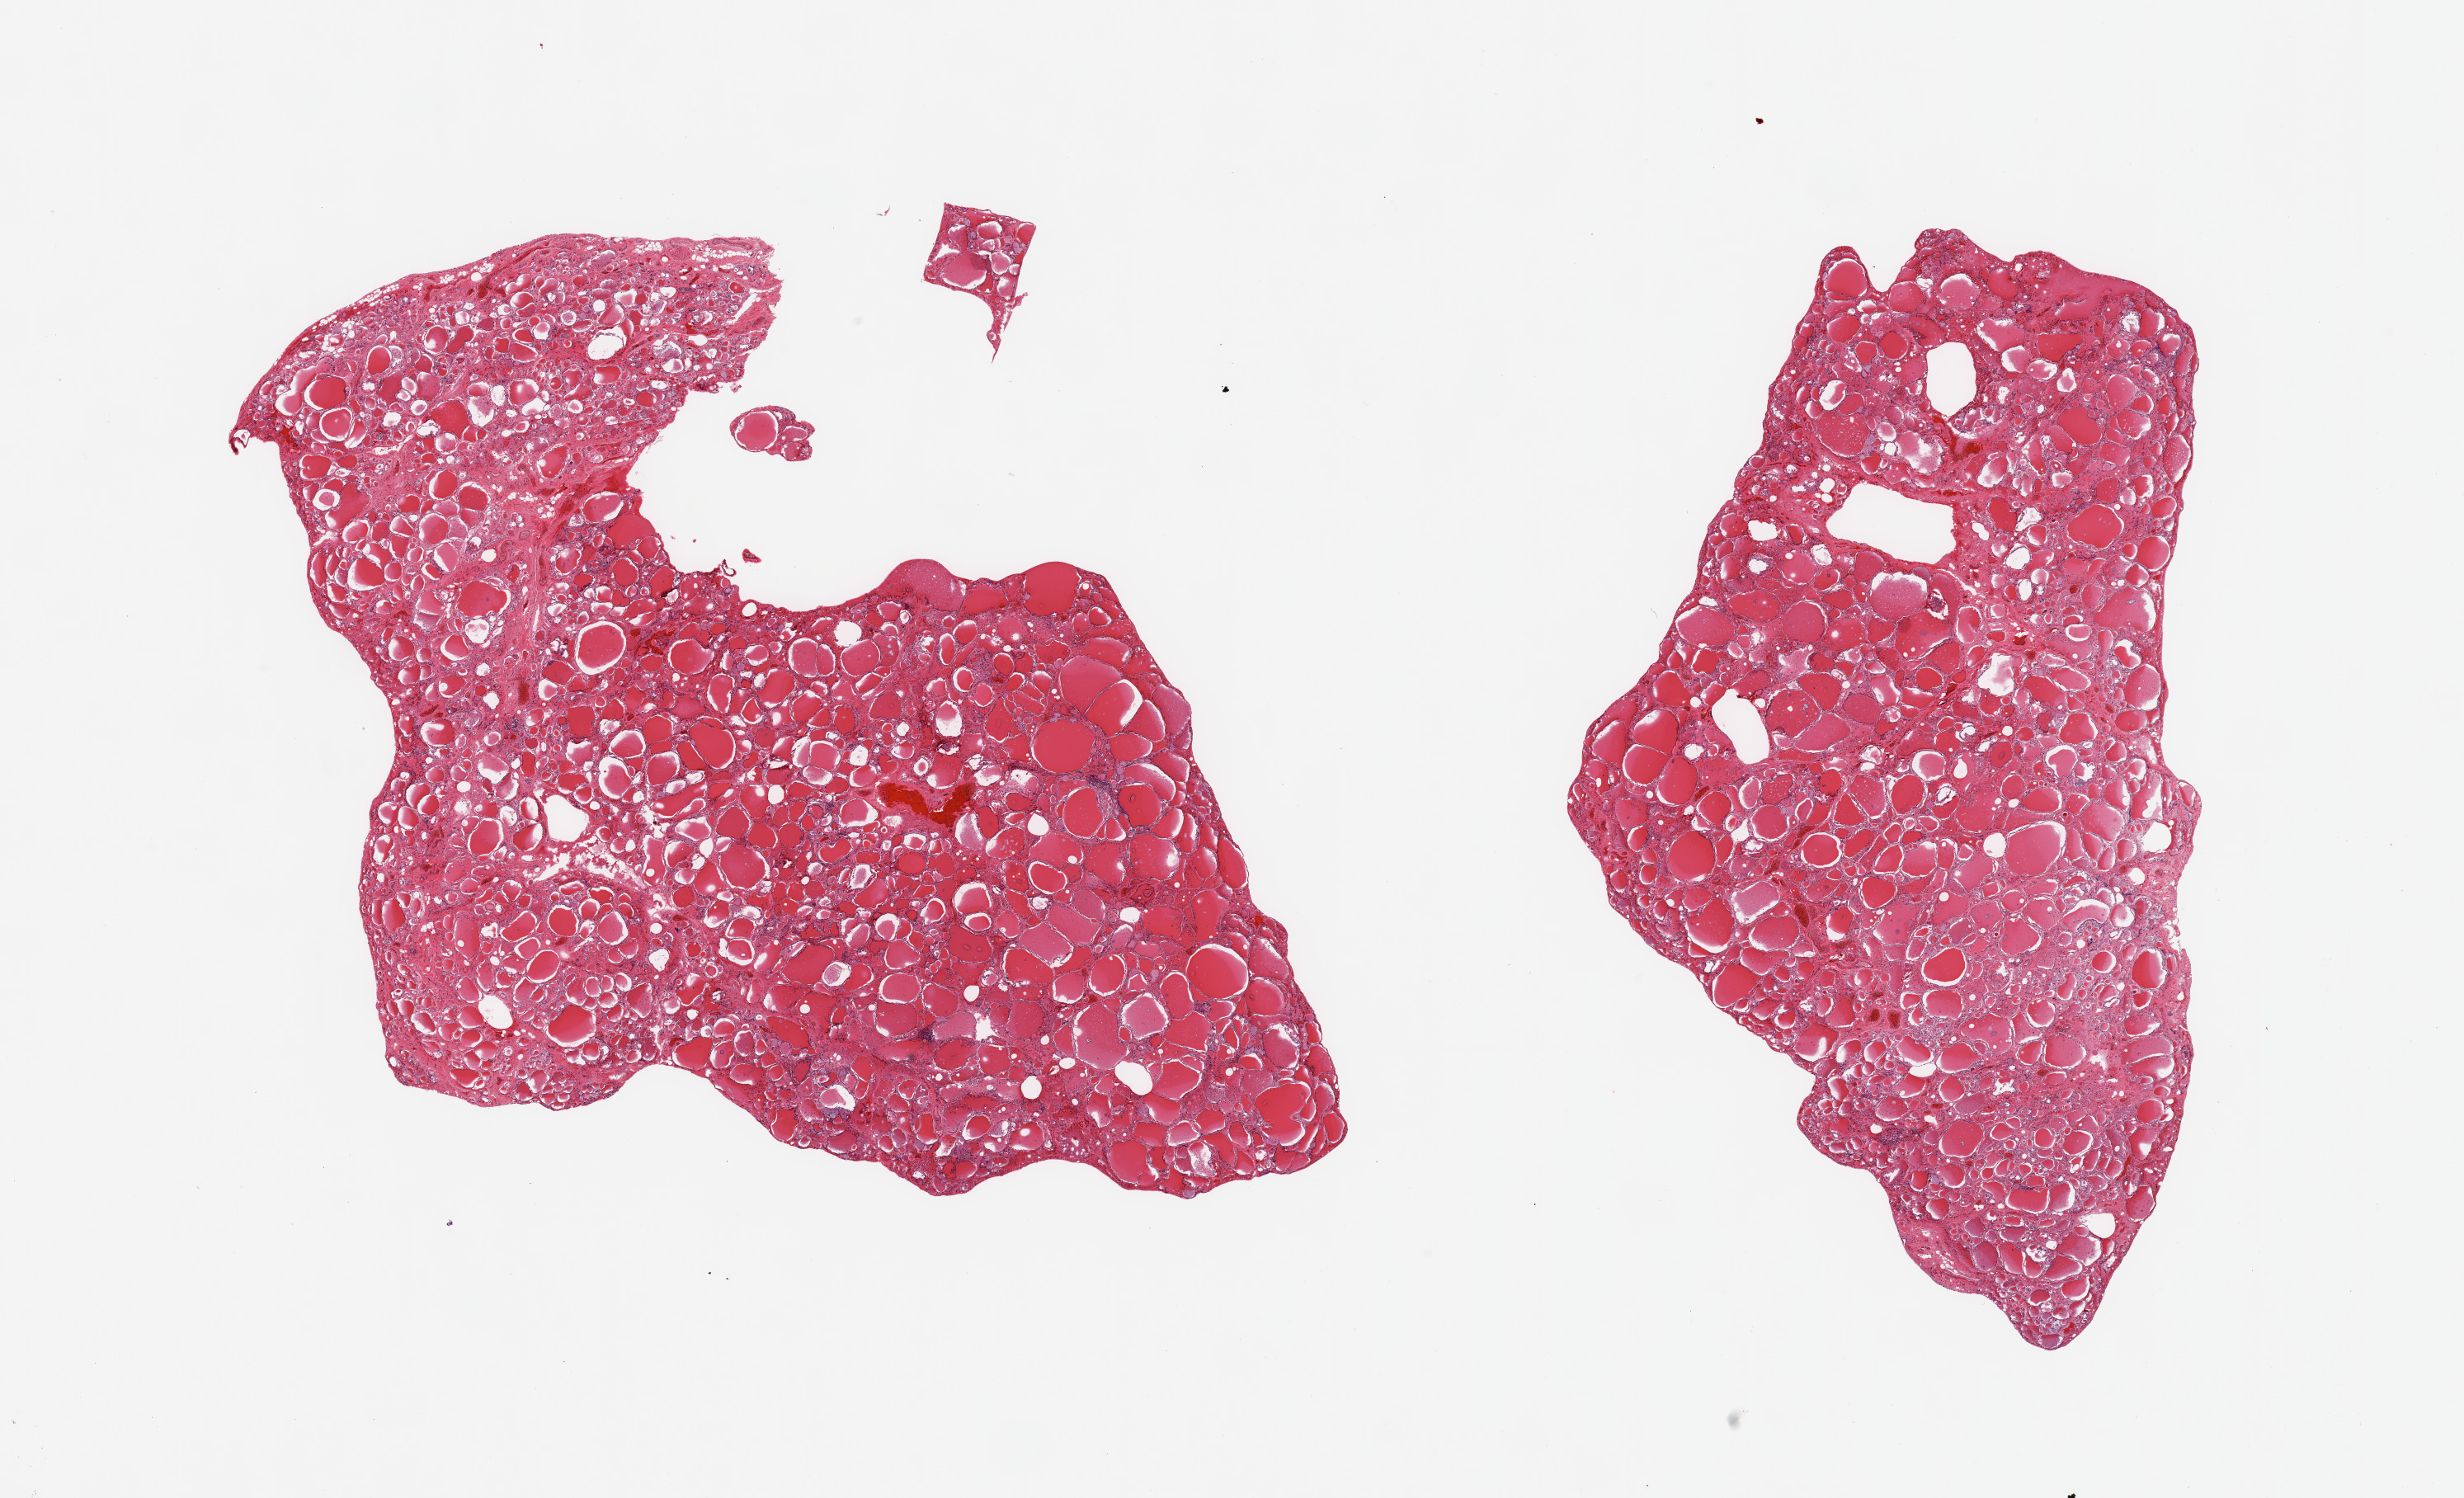
Digitized haematoxylin and eosin-stained section, low-resolution overview of the scanned area, about 23.6 x 14.4 mm; PAXgene-fixed paraffin-embedded (PFPE) section; sampled site (target tissue): thyroid; donor tissue sample. Donor sex: male.
Pathologist's review note for this sample: 2 pieces, no significant abnormalities.